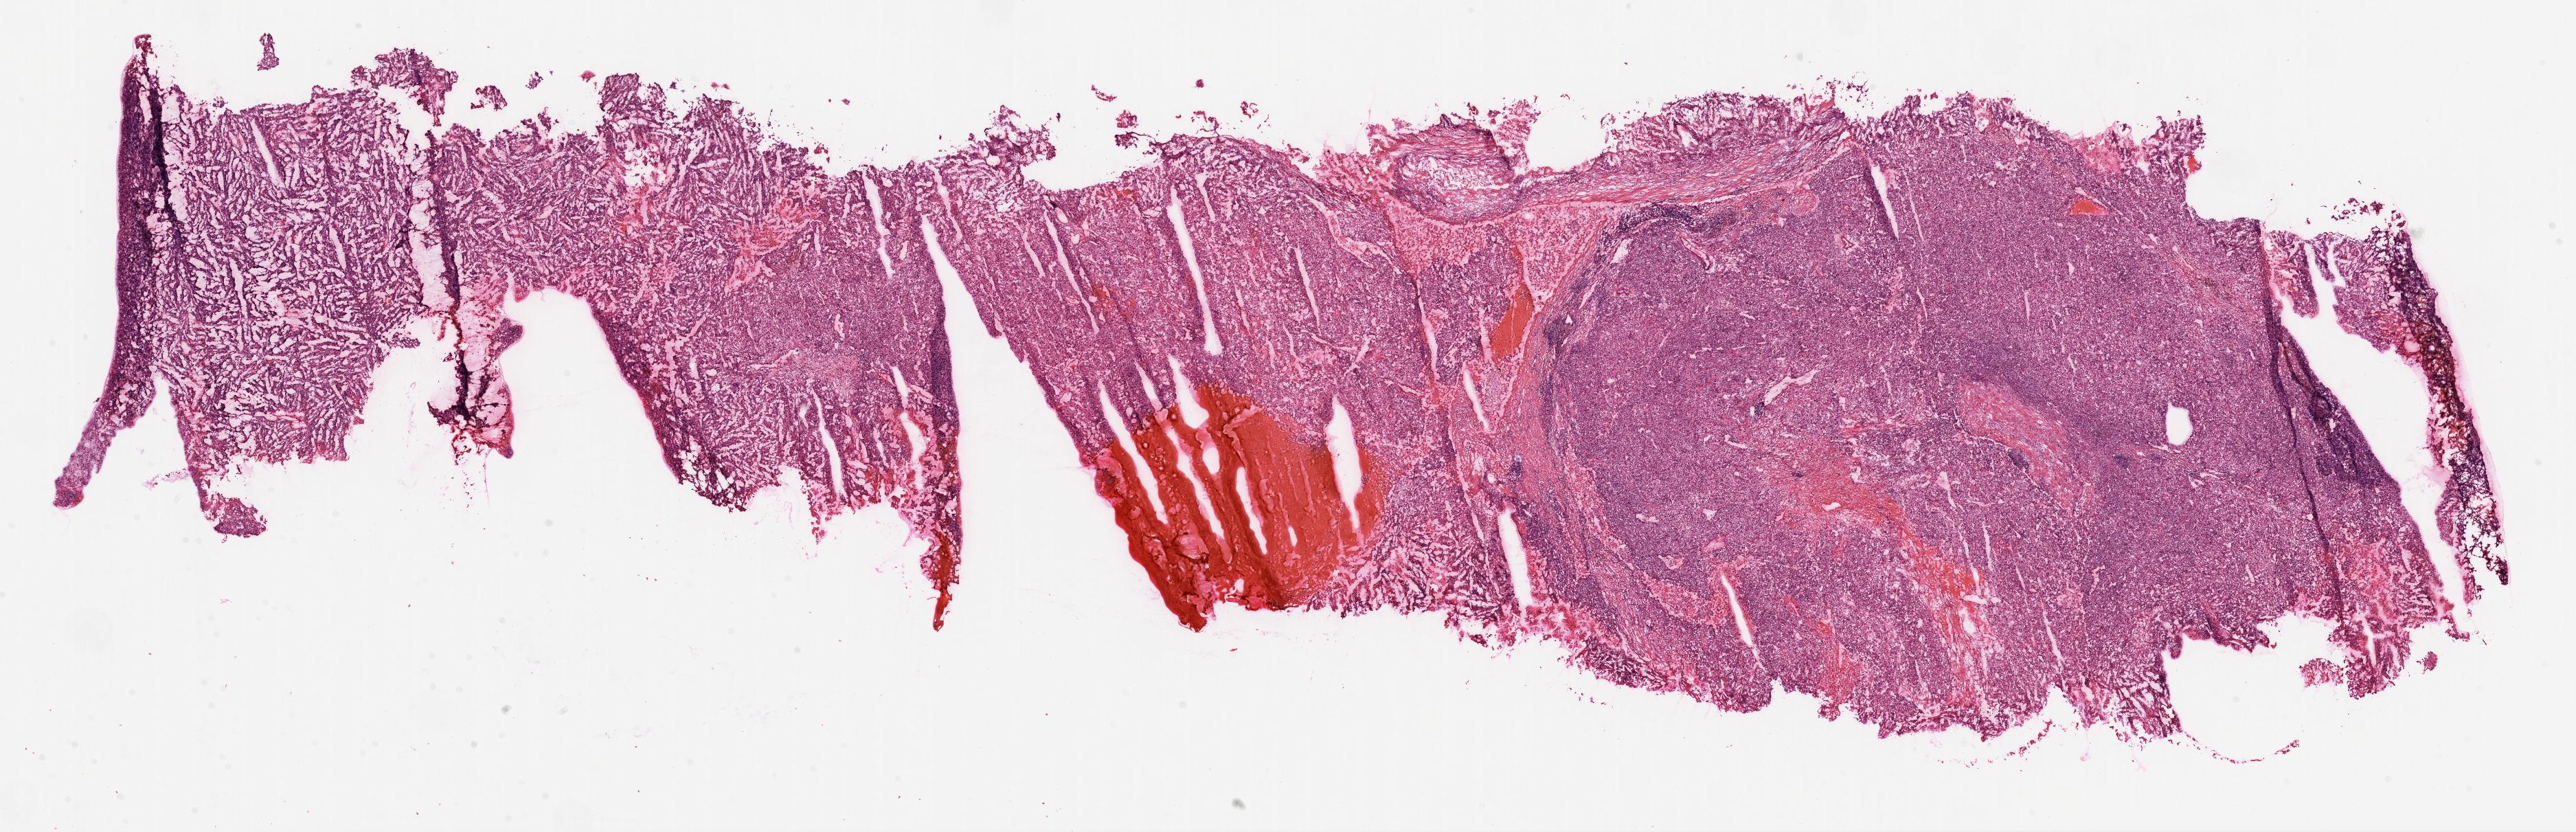
Whole-slide histology image, Hematoxylin and eosin (H&E) stained, low-resolution overview of the scanned area, about 30.1 x 9.7 mm (slide scanned at 20x). Frozen section from the top of the tissue portion. Sample: primary tumour, kidney. Patient sex: female. Histologic grade: G3 (poorly differentiated). Slide review estimates, as recorded: tumour cells 90%, tumour nuclei 90%, normal cells 0%, stromal cells 10%, necrosis 0%.
Pathologic diagnosis: Clear cell adenocarcinoma, NOS. Lymph nodes positive (case pathology): 0 of 3 examined. AJCC pathologic stage: III. Laterality: right.